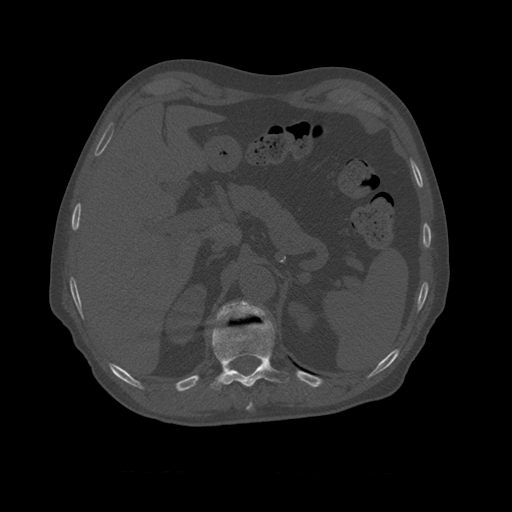
CT including the spine, one axial slice; bone window (W 1800 / L 400 HU); 1.25 mm slice thickness; 512 × 512 image matrix, field of view 405 × 405 mm. Patient age 75 years. Case-level facts recorded for this patient, not image findings: primary cancer: prostate.
Annotated regions visible in this slice (semi-automatically segmented with operator editing):
- T10 vertebra: box from (x=209, y=318) to (x=290, y=391) px
- T11 vertebra: (x=211, y=301)–(x=270, y=325)
- T9 vertebra: (x=247, y=402)–(x=253, y=409)